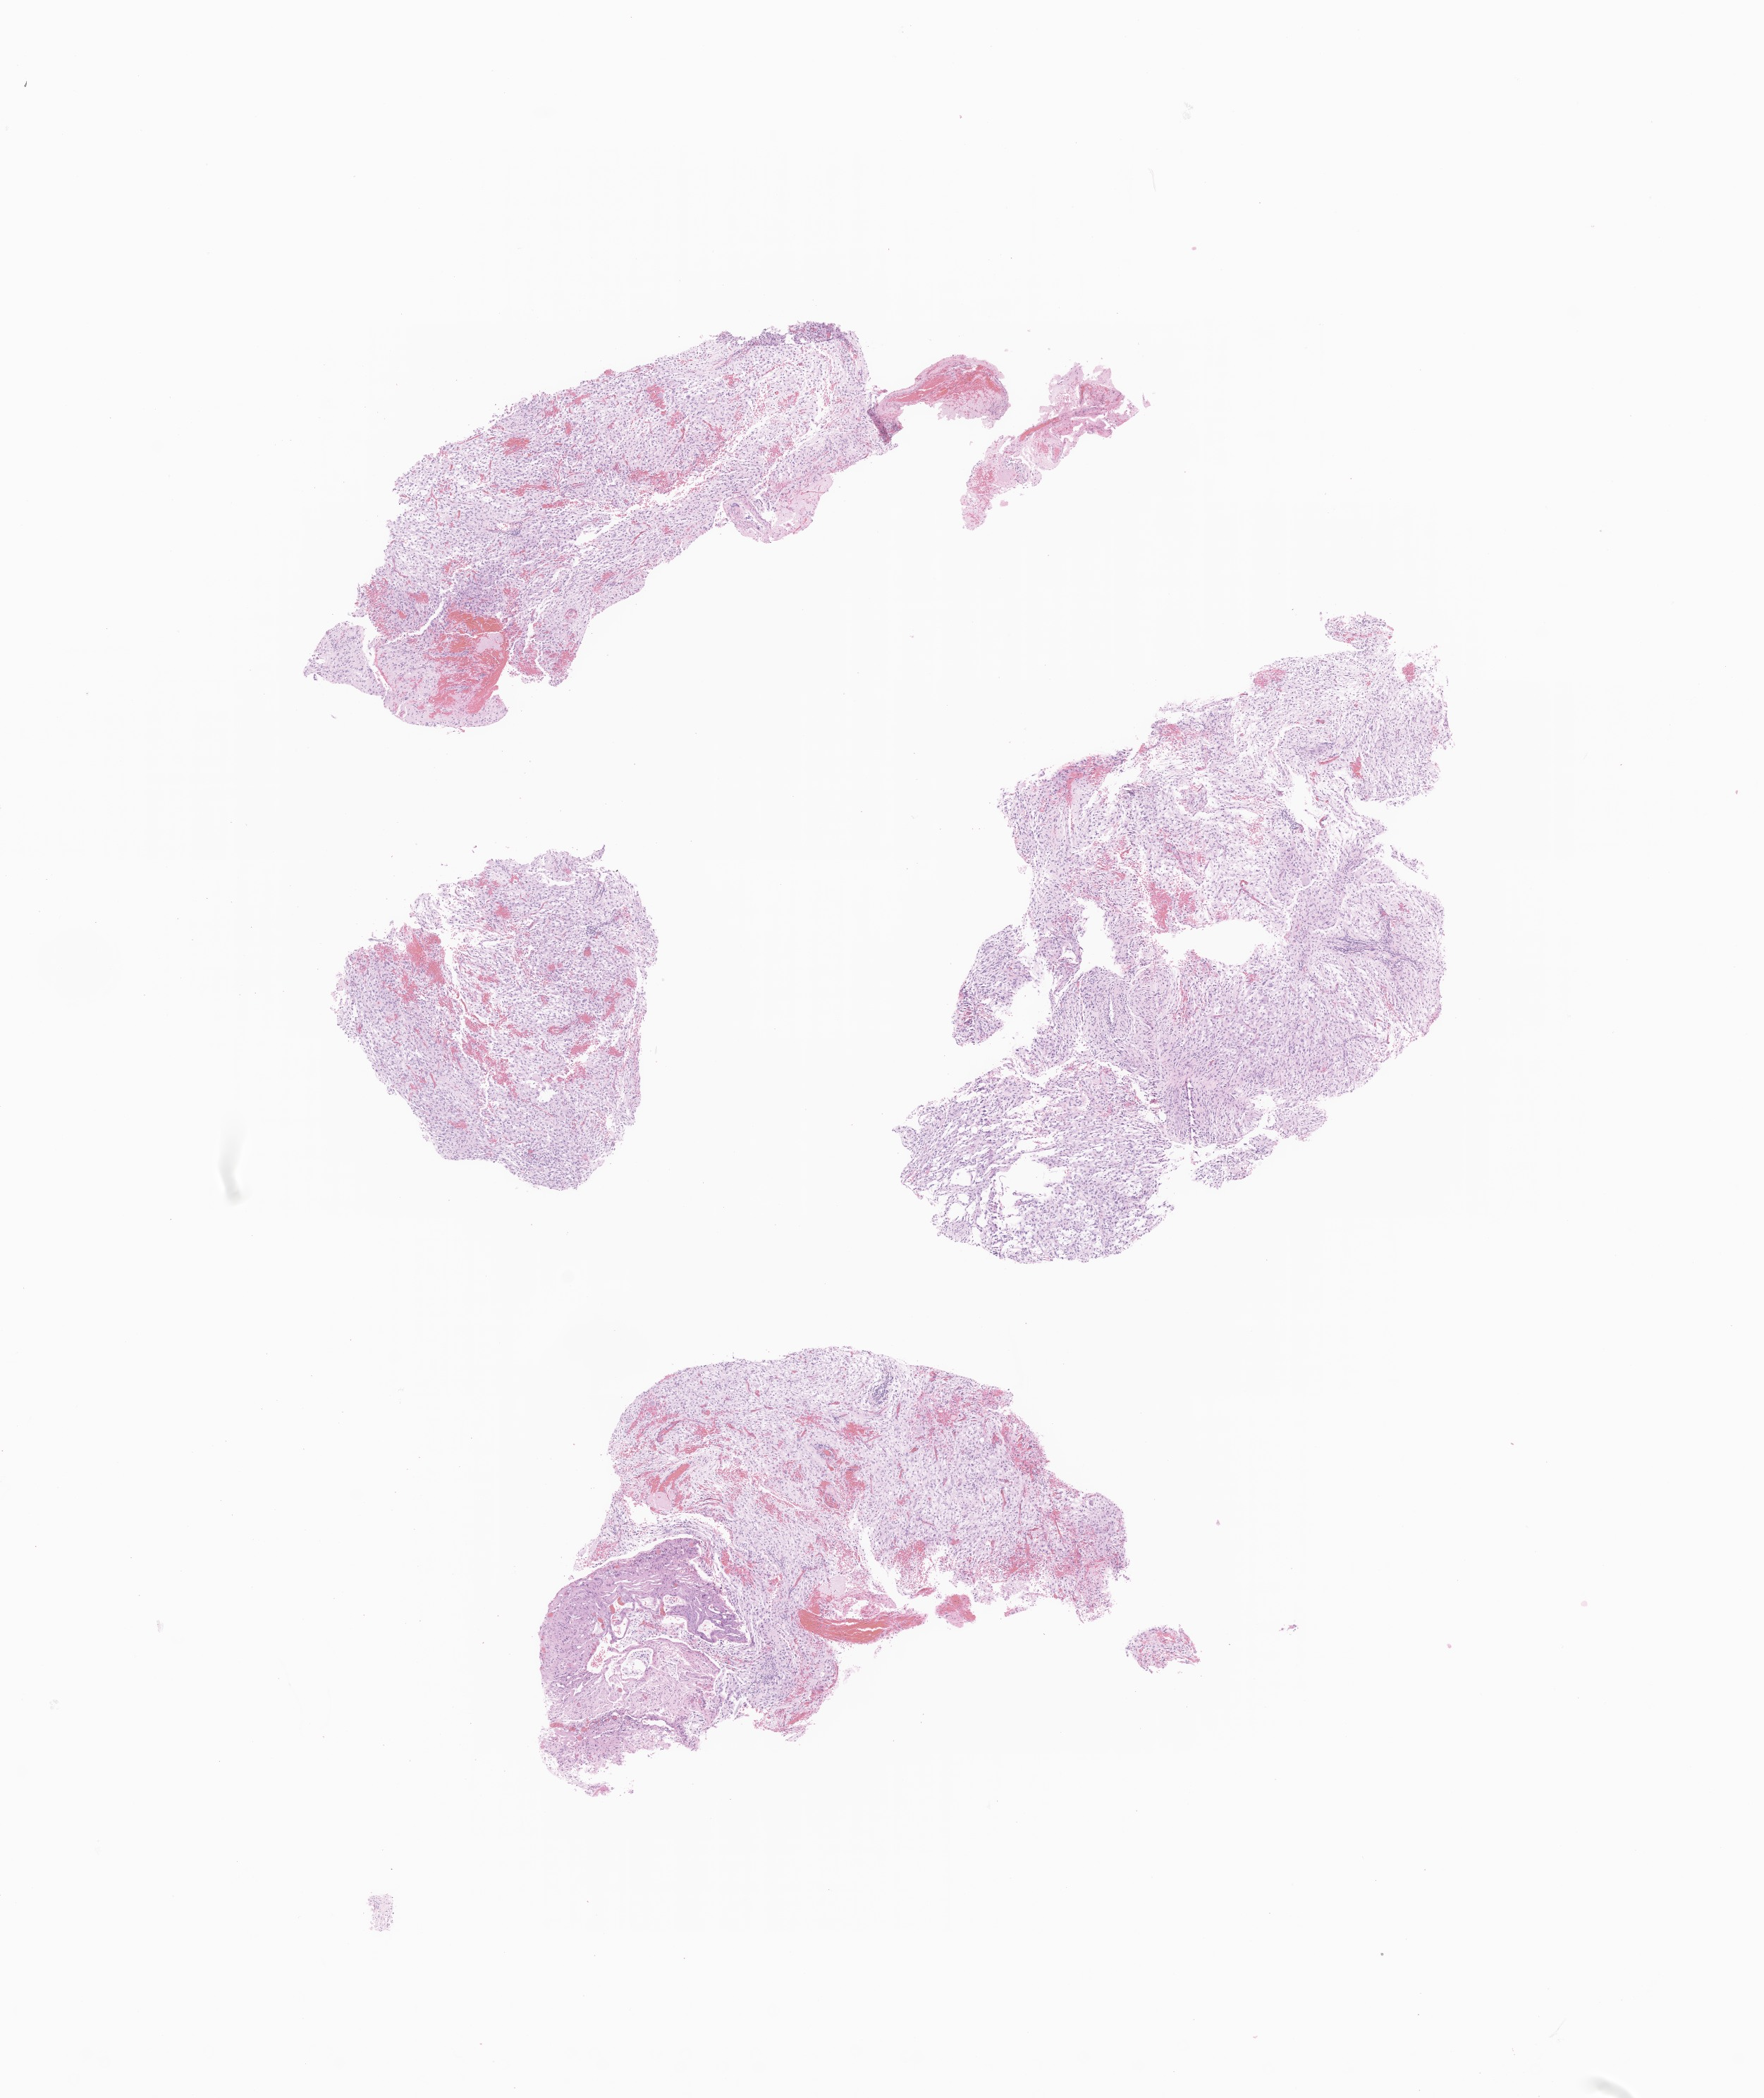
Digitized H&E-stained section of tumor tissue from the brain — a low-resolution overview of the entire scanned area, about 10.5 x 12.5 mm, formalin-fixed paraffin-embedded section. Patient: female, age 130 months (10 years 10 months).
Recorded diagnosis: Ganglioglioma, NOS.